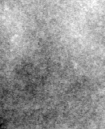
Region of interest cut from a scanned film mammogram (one marked finding); right breast; CC view.
Finding: calcifications, morphology pleomorphic, distribution clustered; BI-RADS assessment category 4; subtlety rating 3 on a 1 (subtle) to 5 (obvious) scale; pathology (as recorded): malignant.